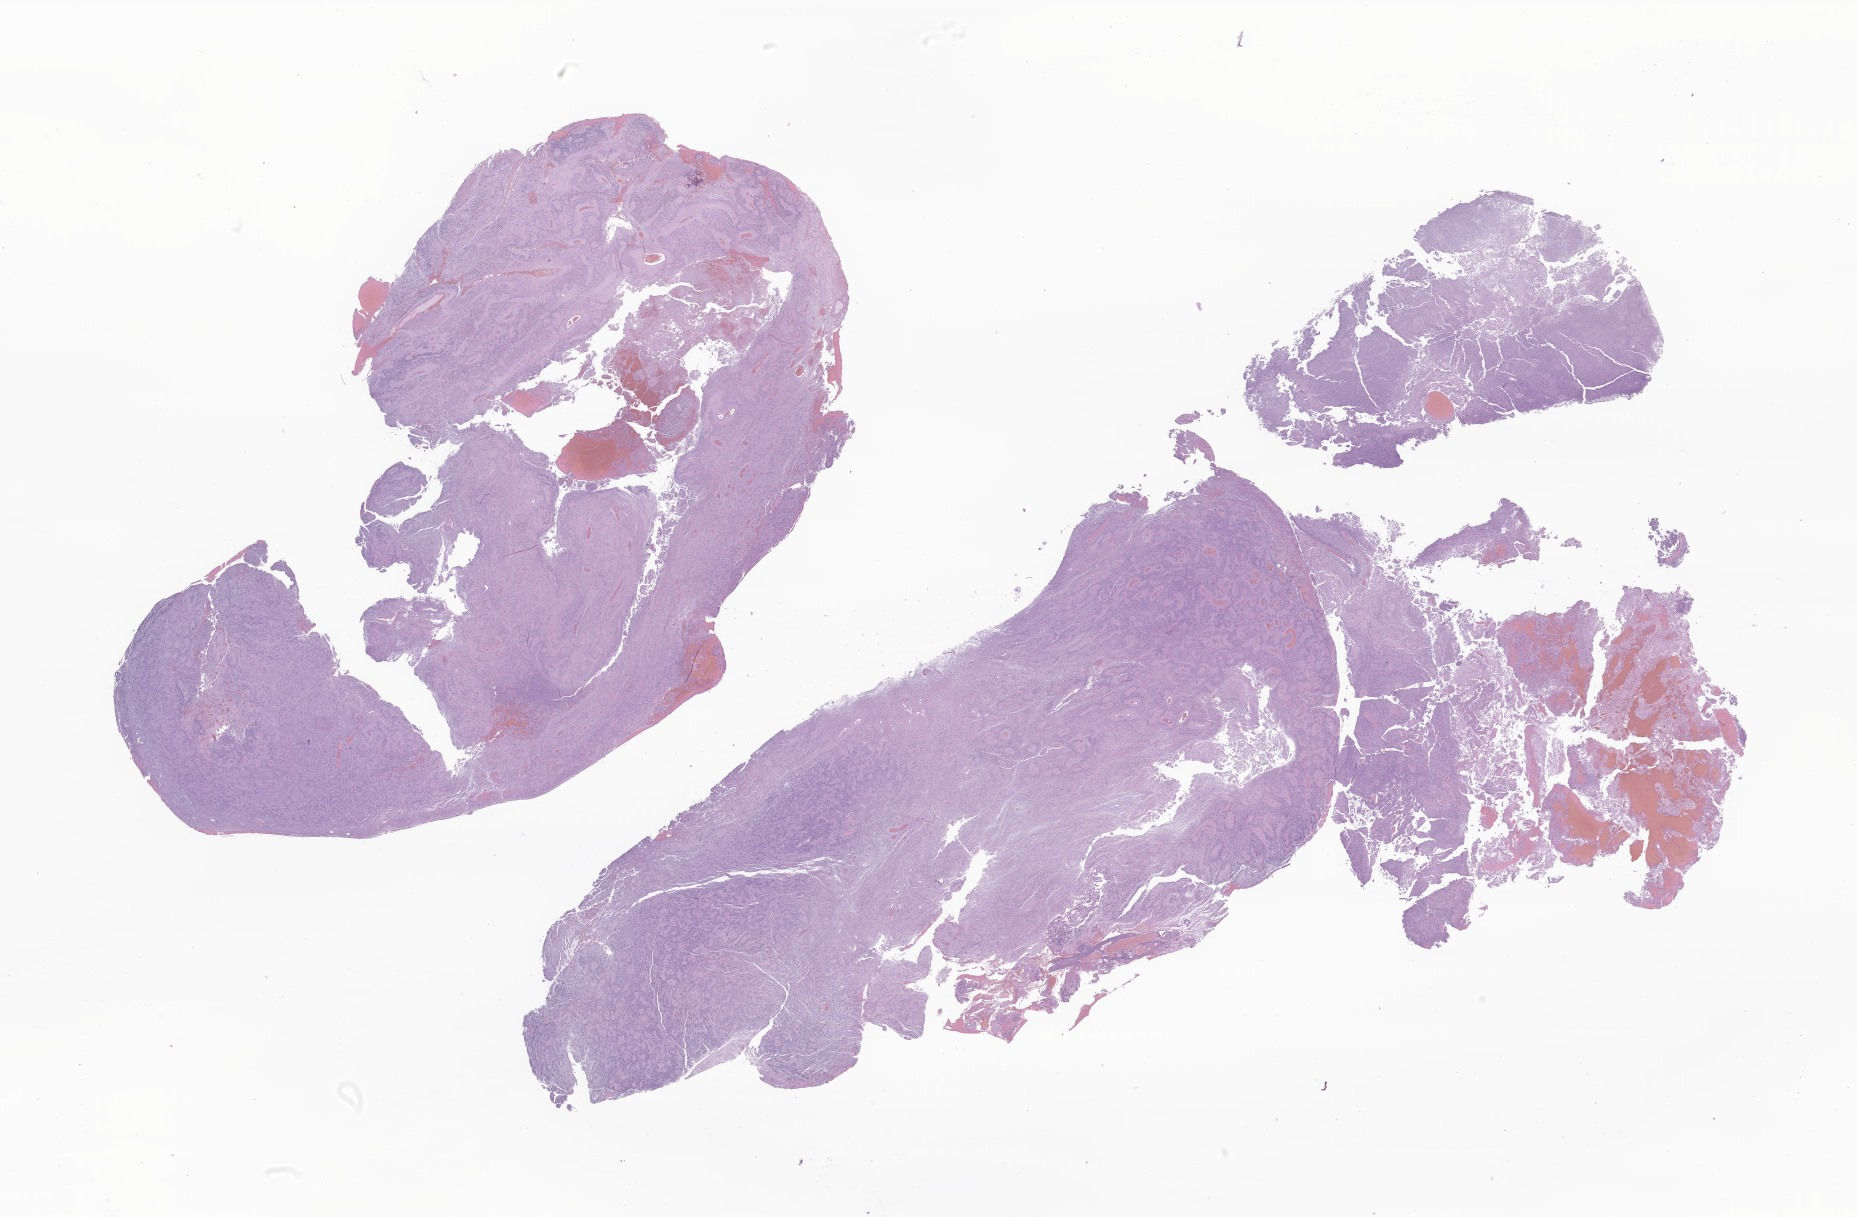
H&E whole-slide image of tumor tissue from the cerebral ventricle, whole scanned area (about 31.3 x 20.5 mm) shown as a low-resolution overview. FFPE section. Female patient, age 645 days (about 1.8 years).
- diagnosis: Ependymoma, NOS